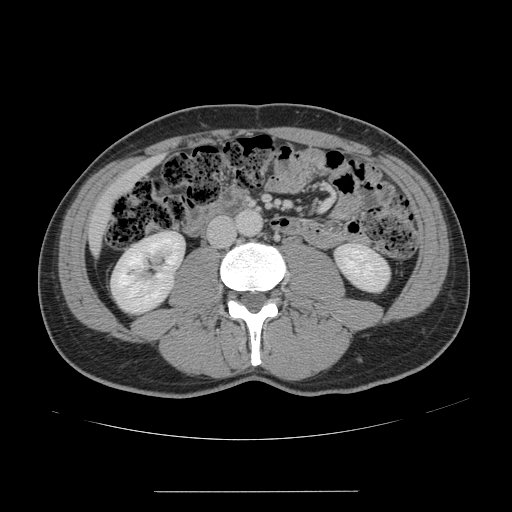
Contrast-enhanced abdominal CT, one axial slice. Intravenous contrast given. Soft-tissue window (W 400 / L 40 HU). 2.5 mm slice thickness. 512 × 512 image matrix. Male patient, age 53 years. Case-level facts recorded for this patient, not image findings: diagnosis: colorectal cancer liver metastases, imaged before liver resection; multiple liver metastases: yes; largest metastasis: 2.4 cm; chemotherapy before resection: yes.
Outlined on this slice (manually delineated by an expert):
- liver: box from (x=91, y=159) to (x=157, y=251) px